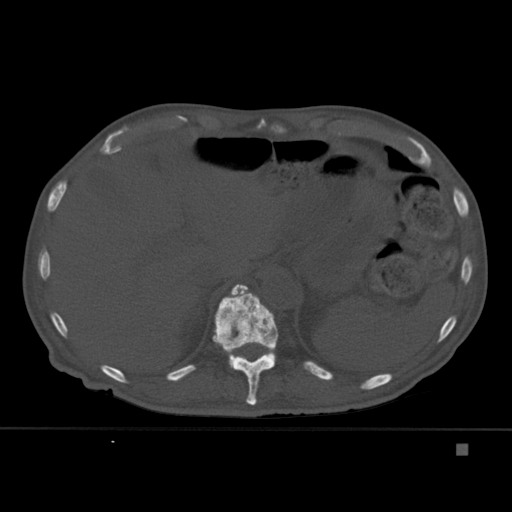
CT including the spine, one axial slice; slice 215 of 451 in the series (ordered by position); bone window (W 1800 / L 400 HU); 1.5 mm slice thickness; 512 × 512 image matrix, field of view 378 × 378 mm. Male patient, age 75 years. From the clinical record (not read from this slice): primary cancer: prostate.
Structures marked on this image (semi-automatic segmentation, software-assisted and operator-edited):
- T11 vertebra: bounding box <212,284,279,405> (left, top, right, bottom; pixels)
- T12 vertebra: <229,284,276,369>